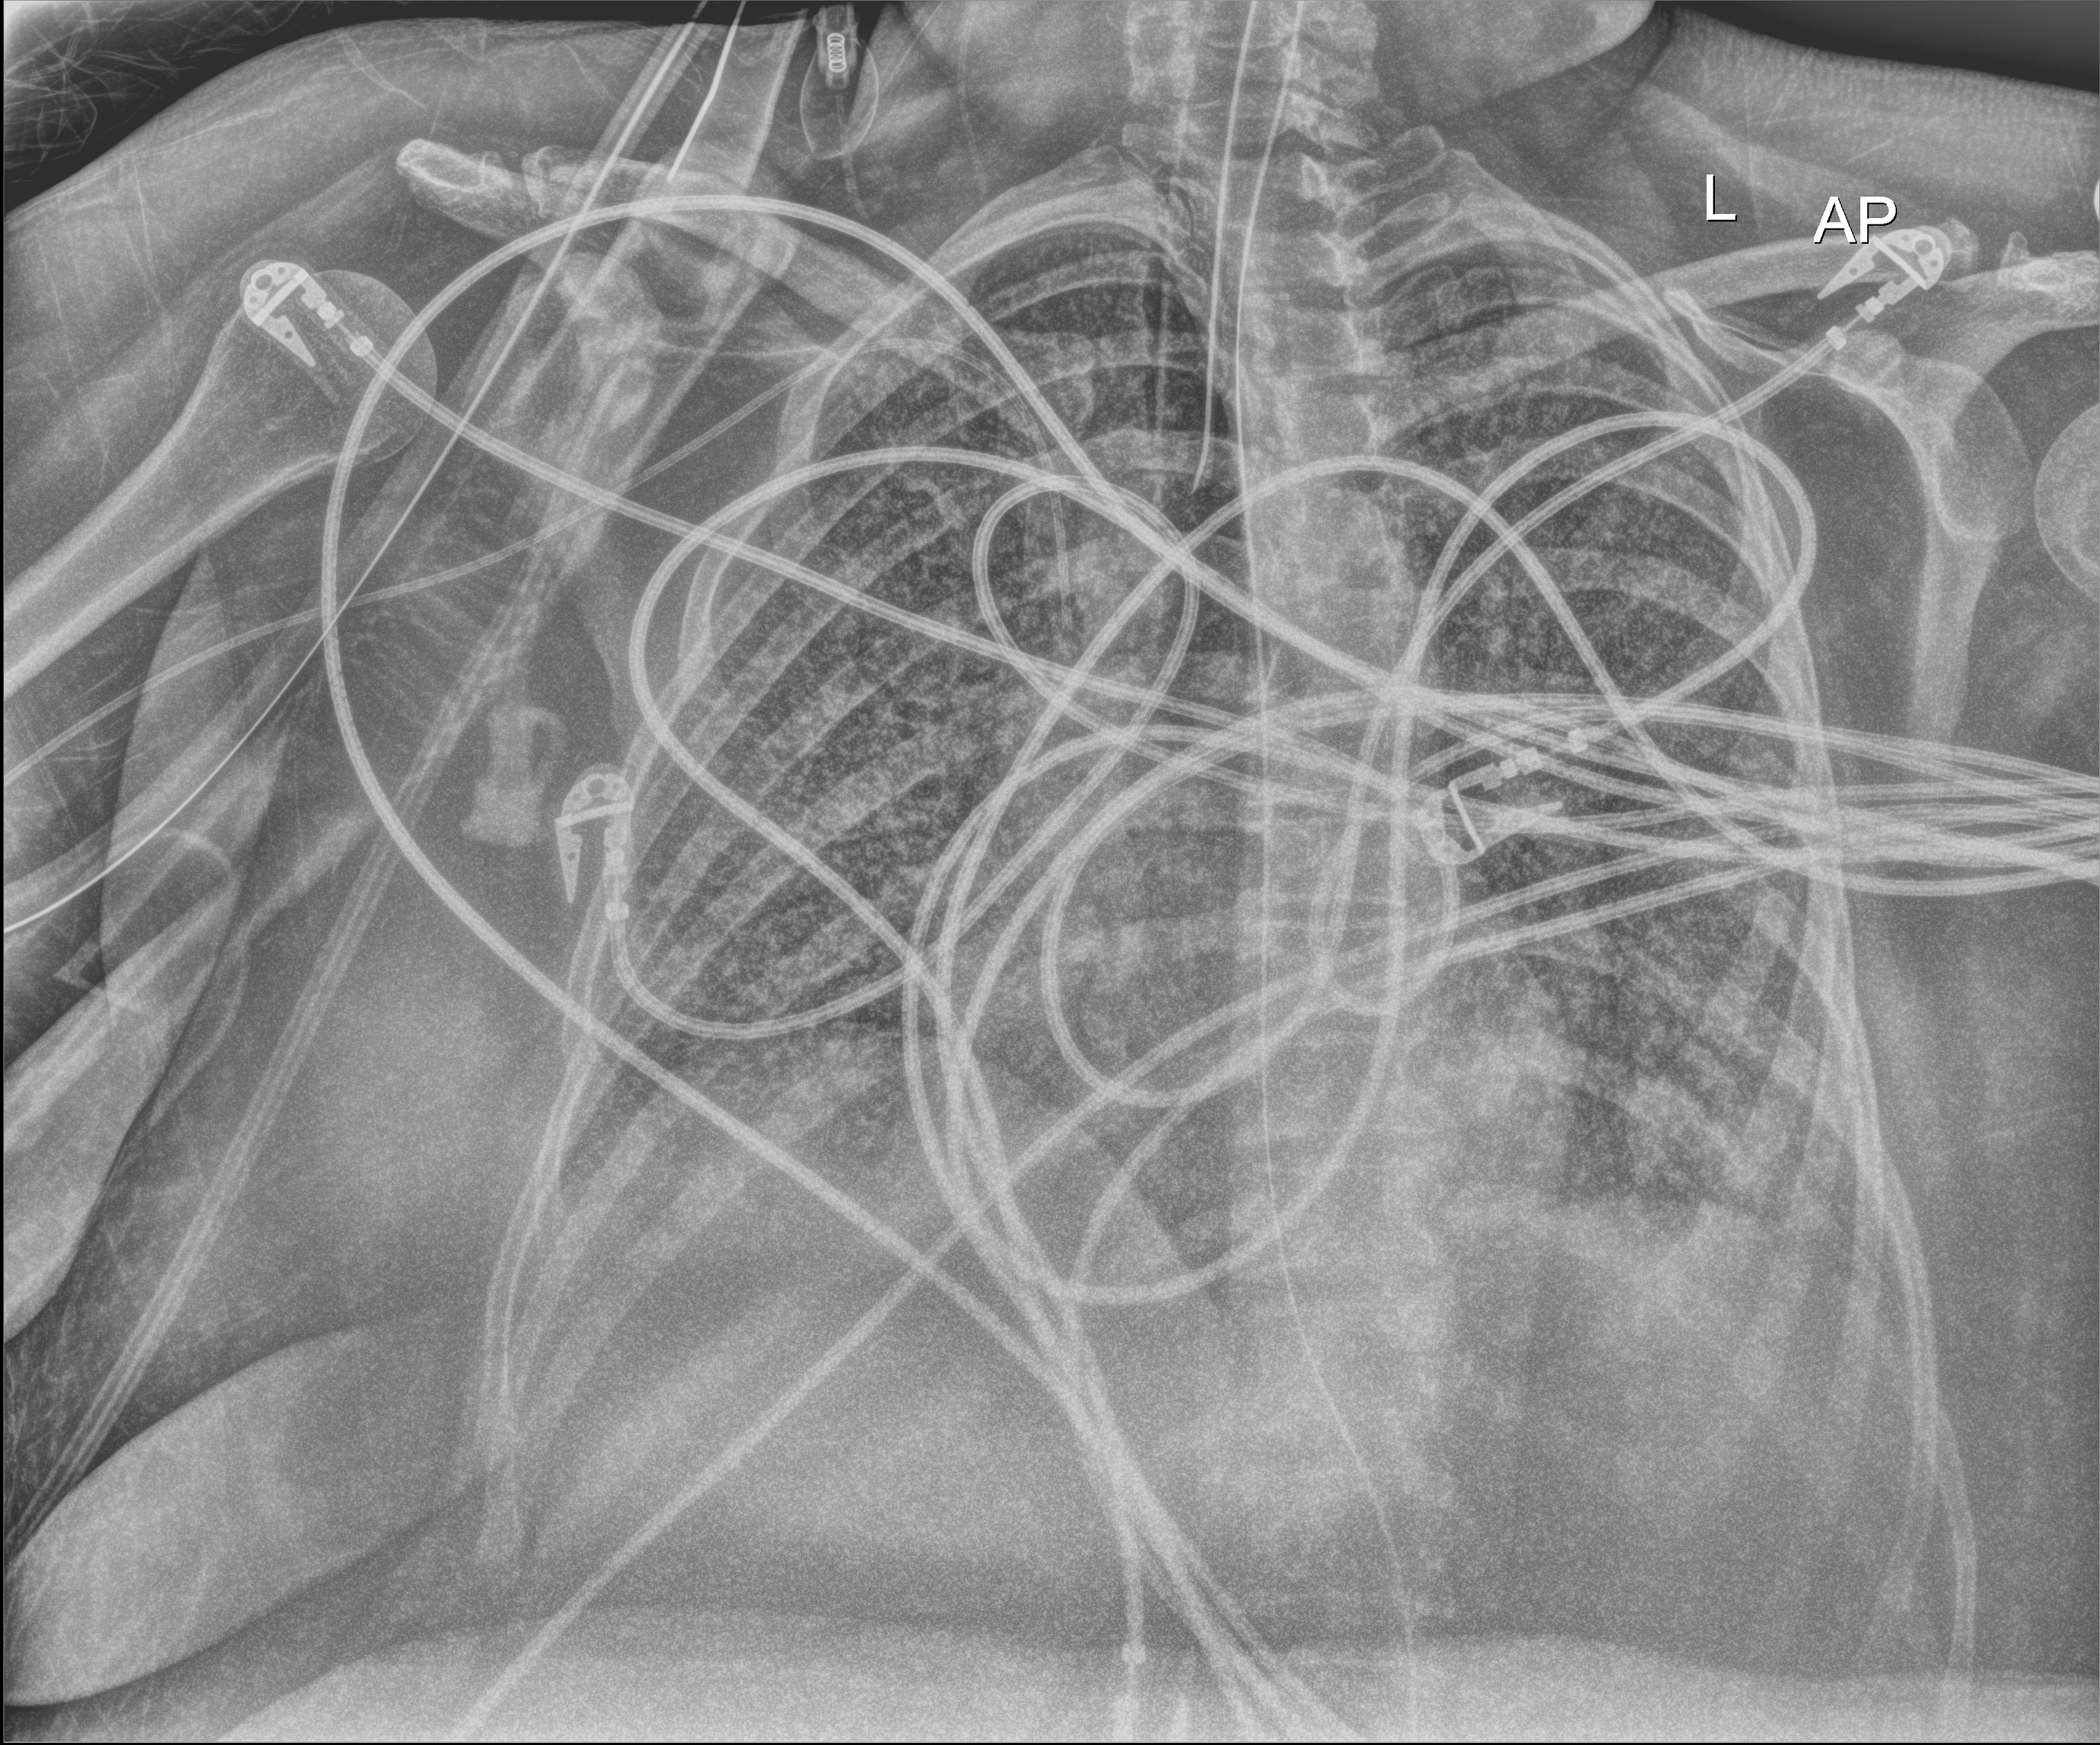
Chest X-ray (portable). Female patient hospitalised with COVID-19, age 18–59 years.
Admission-level facts for this patient (not findings on this image; timing relative to this image not recorded): length of hospital stay: 95 days; mechanically ventilated during this hospital stay: yes.